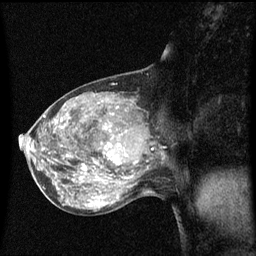
Breast MRI (dynamic contrast-enhanced), one sagittal slice; position 29 of 60 along the scan axis; dynamic contrast-enhanced series, image 2 of 3 at this slice position (ordered by acquisition); 1.5 T; TE 4.2 ms, TR 8.4 ms; 256 × 256 image matrix, field of view 200 × 200 mm. Patient: female, 50 years.
Annotated regions visible in this slice (semi-automatically segmented with operator editing):
- analysis volume of interest (the breast-tissue region the enhancement analysis was run in; not a lesion): box from (x=100, y=114) to (x=153, y=171) px
- tumour enhancement mask (voxels above the 70 % enhancement threshold inside the analysis volume of interest): (x=104, y=124)–(x=136, y=165)